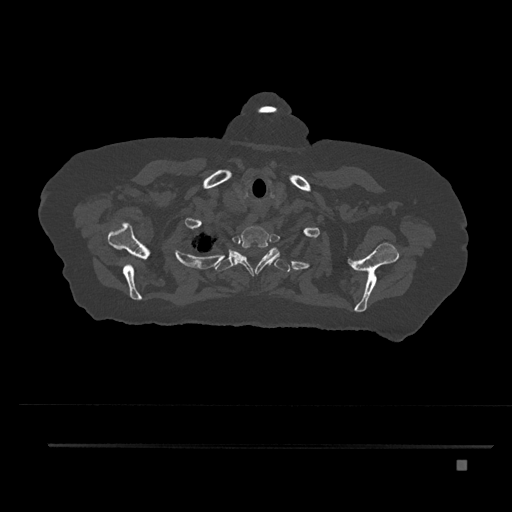
CT including the spine, one axial slice. Slice 687 of 797 in the series (ordered by position). 120 kVp. Bone window (W 1800 / L 400 HU). 512 × 512 image matrix, field of view 437 × 437 mm. Female patient, age 76 years. Case-level facts recorded for this patient, not image findings: primary cancer: lung; vertebrae with lytic lesions (as recorded): T11, L3.
Outlined on this slice (semi-automatically segmented with operator editing):
- T1 vertebra: bounding box [x1, y1, x2, y2] px = [232, 226, 280, 276]
- T2 vertebra: [207, 247, 290, 272]